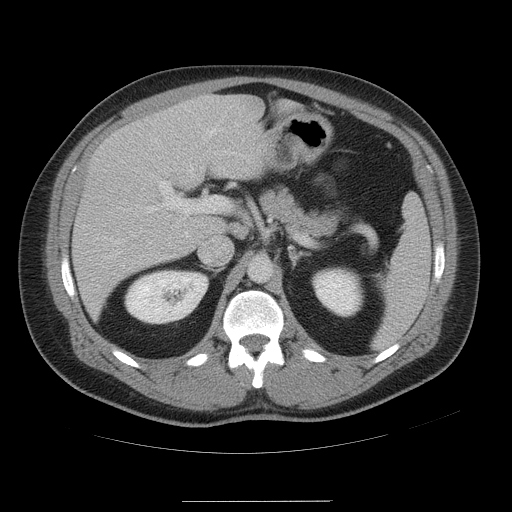
Contrast-enhanced abdominal CT, one axial slice. Slice 30 of 54 in the series (ordered by position). 120 kVp. Intravenous contrast given. Soft-tissue window (W 400 / L 40 HU). 5 mm slice thickness. 512 × 512 image matrix, field of view 436 × 436 mm. Male patient, age 40 years. Case-level facts recorded for this patient, not image findings: diagnosis: colorectal cancer liver metastases, imaged before liver resection; multiple liver metastases: no; largest metastasis: 15 cm; chemotherapy before resection: no.
Outlined on this slice (expert manual segmentation):
- hepatic veins: bounding box (x1, y1, x2, y2) in pixels: (188, 129, 216, 173)
- liver: (72, 95, 282, 320)
- planned liver remnant (the part of the liver to remain after resection): (205, 95, 280, 234)
- portal vein (with intrahepatic branches): (147, 181, 231, 228)